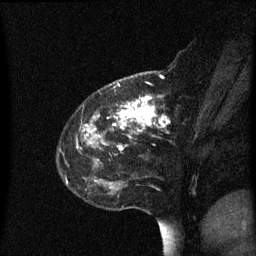
Breast MRI (dynamic contrast-enhanced), one sagittal slice; slice 20 of 60 in the series (ordered by position); dynamic contrast-enhanced series, image 2 of 3 at this slice position (ordered by acquisition); 1.5 T; TE 4.2 ms, TR 8.4 ms; 2 mm slice thickness; 256 × 256 image matrix, field of view 200 × 200 mm. Female patient, age 48 years. Case-level facts recorded for this patient, not image findings: setting: breast cancer imaged before/during neoadjuvant chemotherapy; receptor status: HR-positive, HER2-negative.
Structures marked on this image (semi-automatically segmented with operator editing):
- analysis volume of interest (the breast-tissue region the enhancement analysis was run in; not a lesion): bounding box [x1, y1, x2, y2] px = [80, 78, 195, 214]
- tumour enhancement mask (voxels above the 70 % enhancement threshold inside the analysis volume of interest): [86, 96, 171, 183]